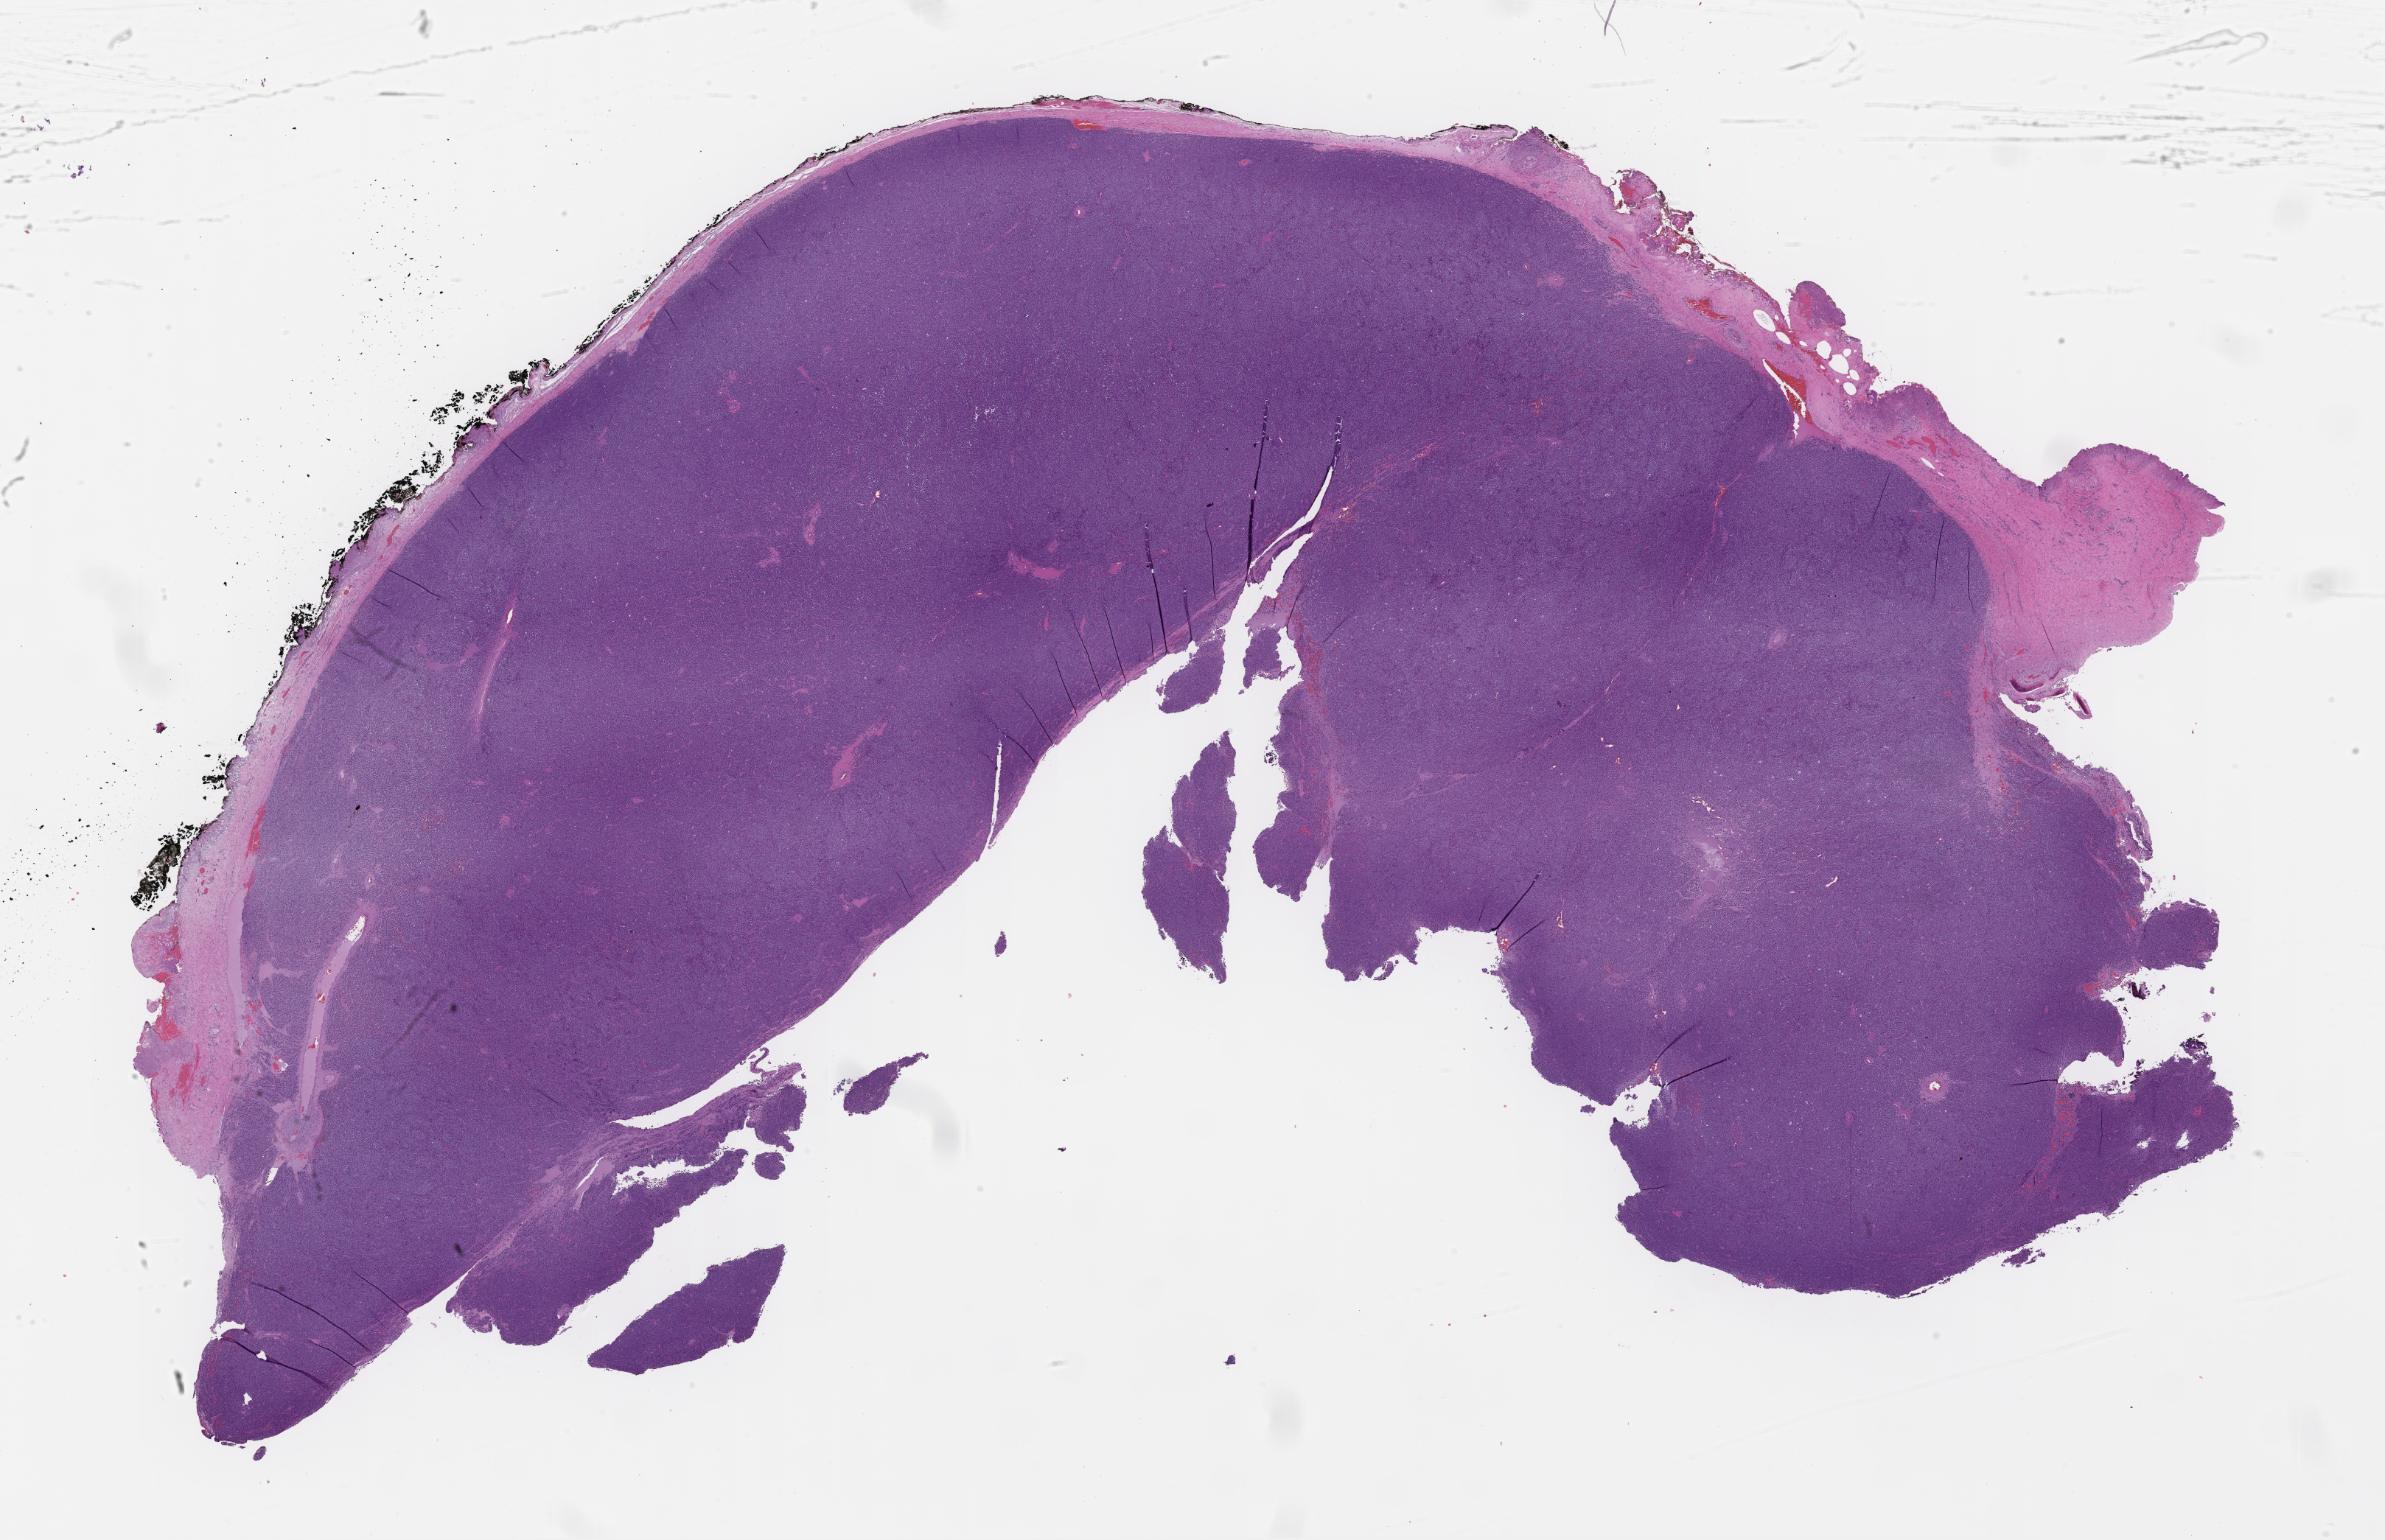
Whole-slide image, hematoxylin and eosin (H&E) stain, whole scanned area (about 26.1 x 16.9 mm) shown as a low-resolution overview, formalin-fixed paraffin-embedded section, archival tissue. Male patient.
* this section: metastasis (sampled organ not recorded)
* primary diagnosis of the patient: Plasma Cell Myeloma